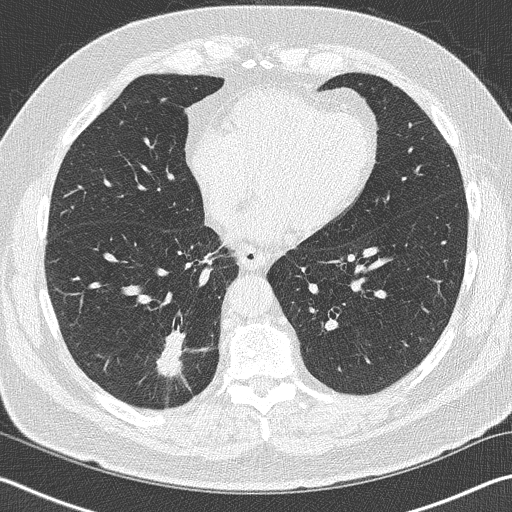
Axial slice from a low-dose chest CT screening exam. First (baseline) screen. Lung window (W 1500 / L -600 HU). Slice 101 of 141 in the series. 512 × 512 image matrix, field of view 344 × 344 mm. Male, age 70 years at enrolment. Current smoker at enrolment.
Expert-annotated lung lesion, bounding box <140,325,211,399> (left, top, right, bottom; pixels). The exam's reader record, not a measurement of the box and not confirmed to be the same lesion: non-calcified nodule or mass ≥4 mm, right lower lobe, 28 × 23 mm, spiculated (stellate) margins, soft tissue attenuation. Participant outcome: lung cancer diagnosed 62 days after this screen — squamous cell carcinoma, NOS, right lower lobe, poorly differentiated (G3), stage IB (AJCC 6th edition), 24 mm at pathology.